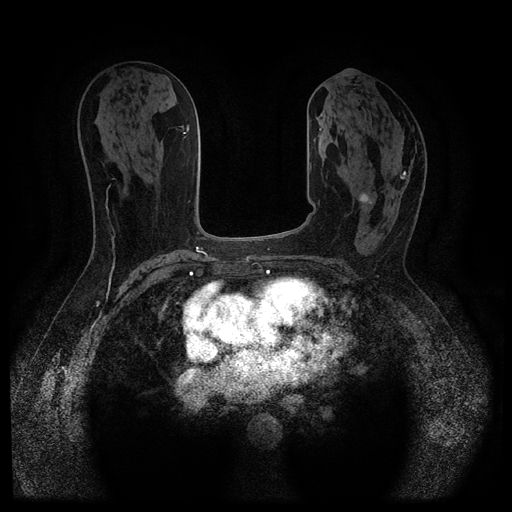
Breast MRI (dynamic contrast-enhanced, multi-phase), one axial slice; slice 51 of 116 in the series (ordered by position); dynamic contrast-enhanced series, time point 2 of 5 at this slice position (early post-contrast); 1.5 T; TE 2.6 ms, TR 5.4 ms; 2 mm slice thickness; 512 × 512 image matrix, field of view 340 × 340 mm. Patient: female, 64 years.
Annotated regions visible in this slice (semi-automatic segmentation, software-assisted and operator-edited):
- breast lesion (labelled 'tumour' in the annotation; benign lesions carry a separate 'benign' label): bounding box [x1, y1, x2, y2] px = [359, 193, 374, 204]